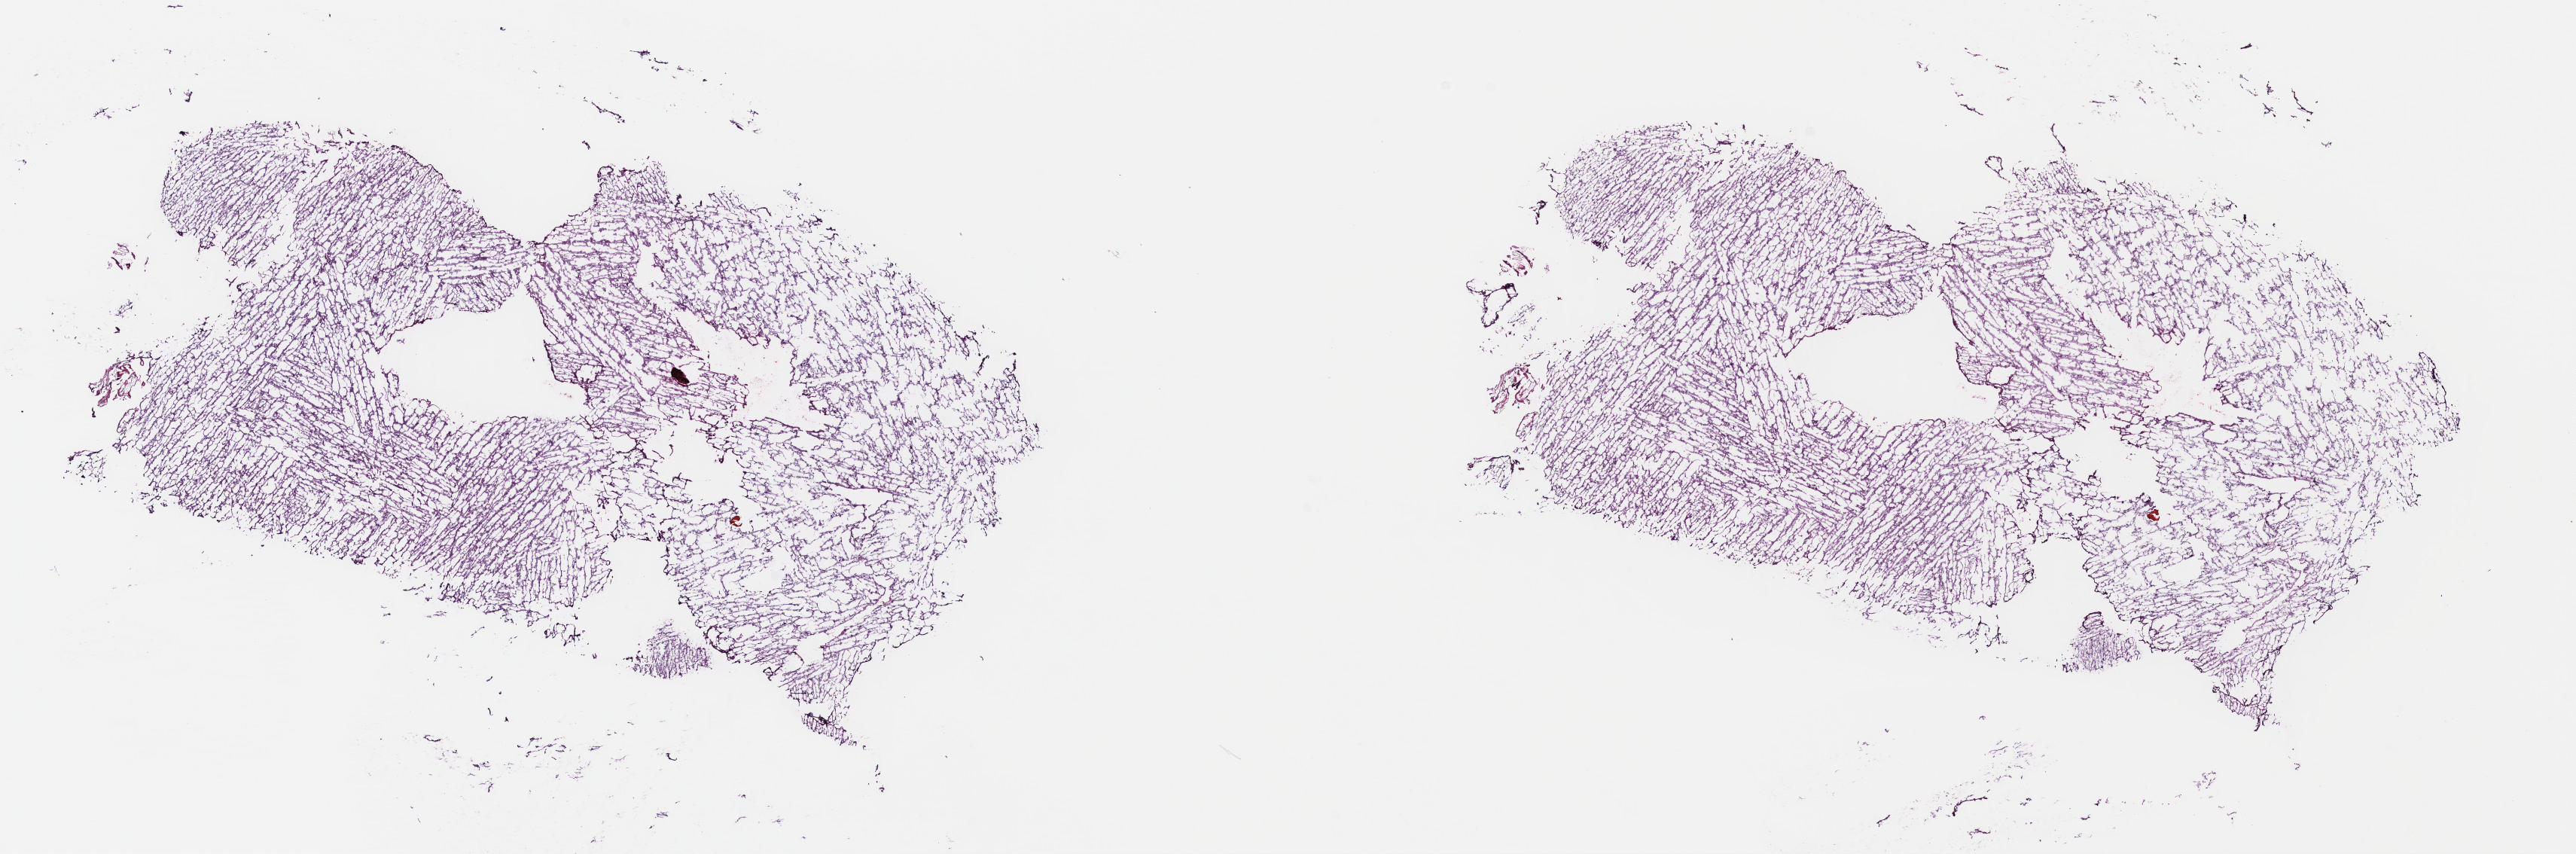
Hematoxylin and eosin (H&E) stained whole-slide image — shown as a low-resolution overview of the whole scanned area (about 26.9 x 8.9 mm); frozen section from the top of the tissue portion; primary tumour sample from the brain. Female, age 52 years at initial diagnosis. Composition of this section per pathologist review: tumour cells 30%, tumour nuclei 70%.
Histologic diagnosis: Astrocytoma, NOS.